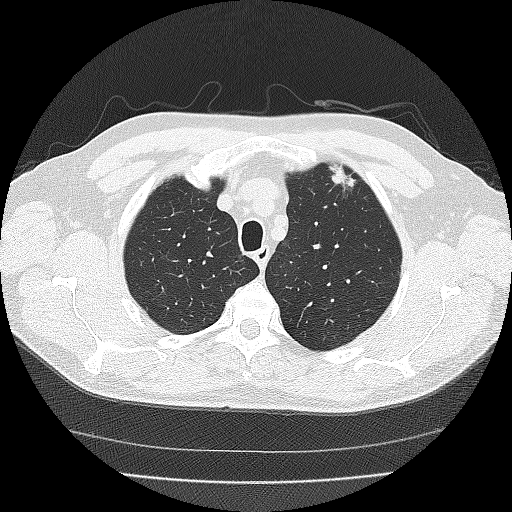
Axial slice from a low-dose chest CT screening exam; third annual screen; lung window (W 1500 / L -600 HU); 2 mm slice thickness; 120 kVp; slice 35 of 167 in the series; 512 × 512 image matrix, field of view 359 × 359 mm. Male, age 56 years at enrolment.
• Expert-annotated lung lesion, bounding box <322,158,364,197> (left, top, right, bottom; pixels).
• The exam's reader record, not a measurement of the box and not confirmed to be the same lesion: non-calcified nodule or mass ≥4 mm, left upper lobe, 18 × 10 mm, spiculated (stellate) margins, soft tissue attenuation, pre-existing on the prior screen: yes; interval growth: yes.